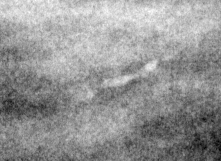
Crop from a digitized film mammogram around one marked abnormality, left breast, MLO view.
Finding: calcifications, morphology fine linear branching, distribution linear; BI-RADS assessment category 4; subtlety rating 2 on a 1 (subtle) to 5 (obvious) scale; pathology (as recorded): malignant.